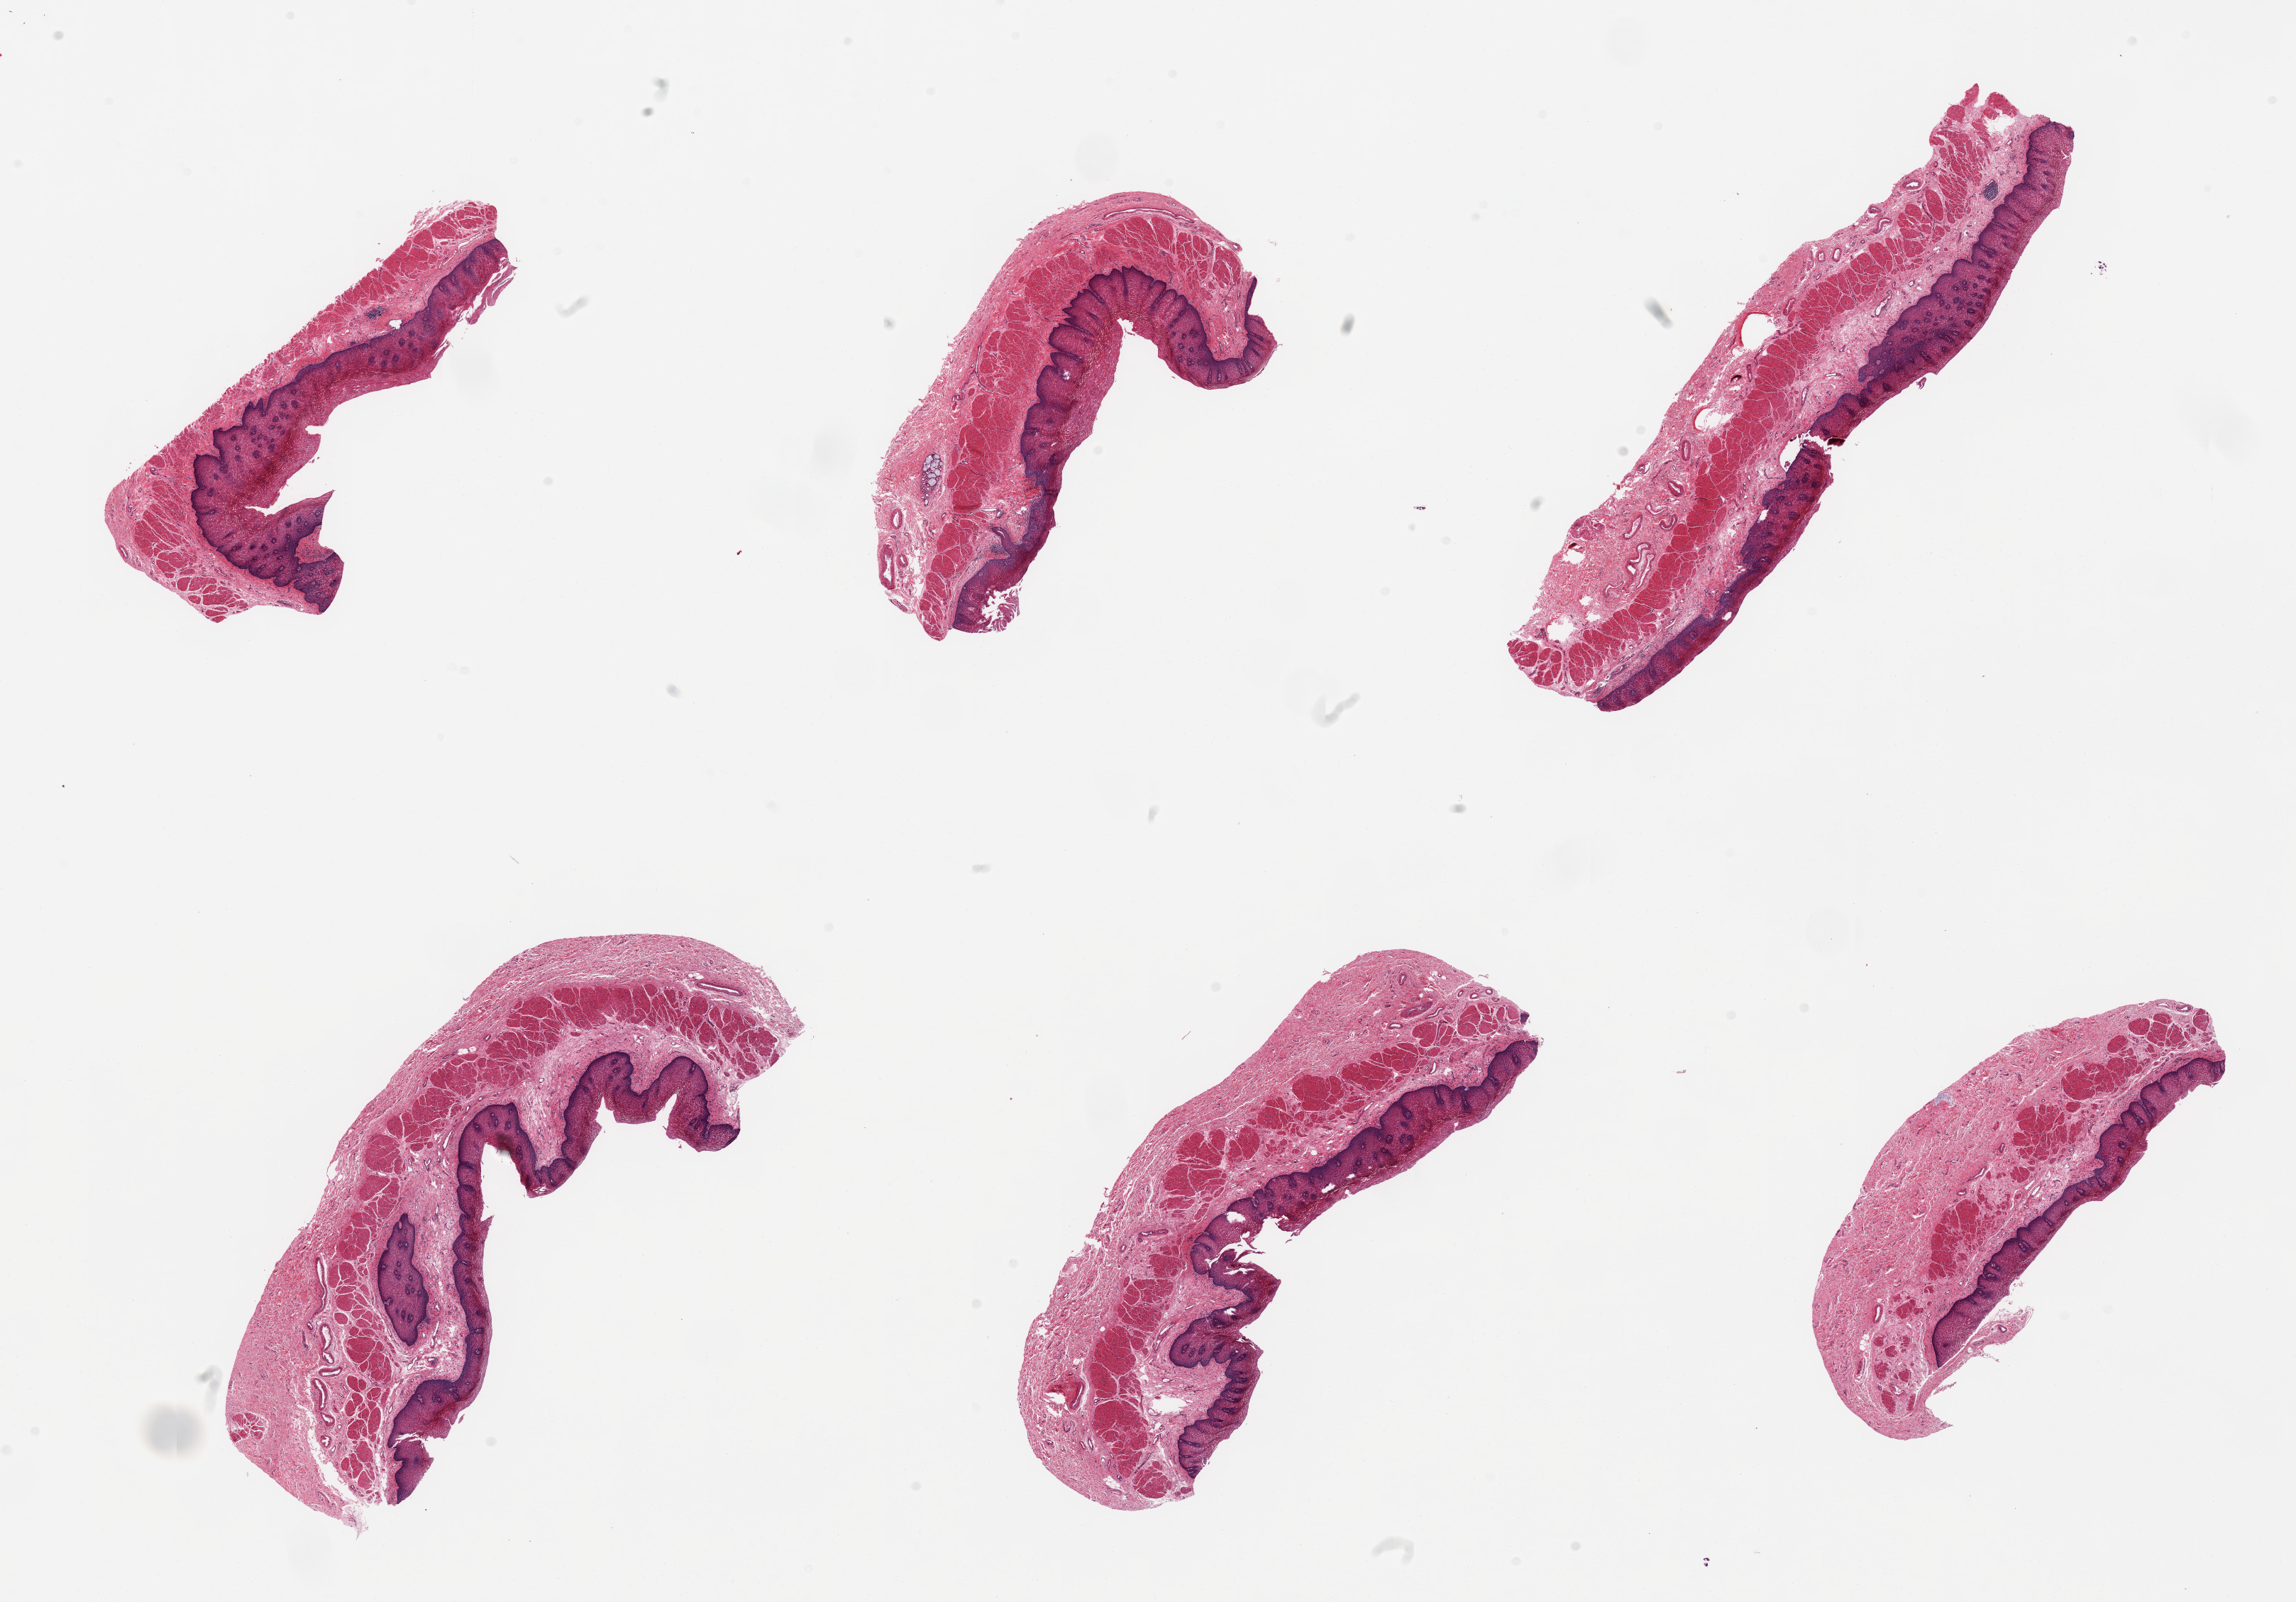
Digitized haematoxylin and eosin-stained section, a low-resolution overview of the entire scanned area, about 25.6 x 17.9 mm. PAXgene-fixed, paraffin-embedded tissue. Target tissue: esophageal mucous membrane. Tissue donor sample. Donor sex: female.
- pathologist's review note for this sample: 6 pieces, squamous mucosa hyperplastic, up to 0.8mm, 20-40% thickness